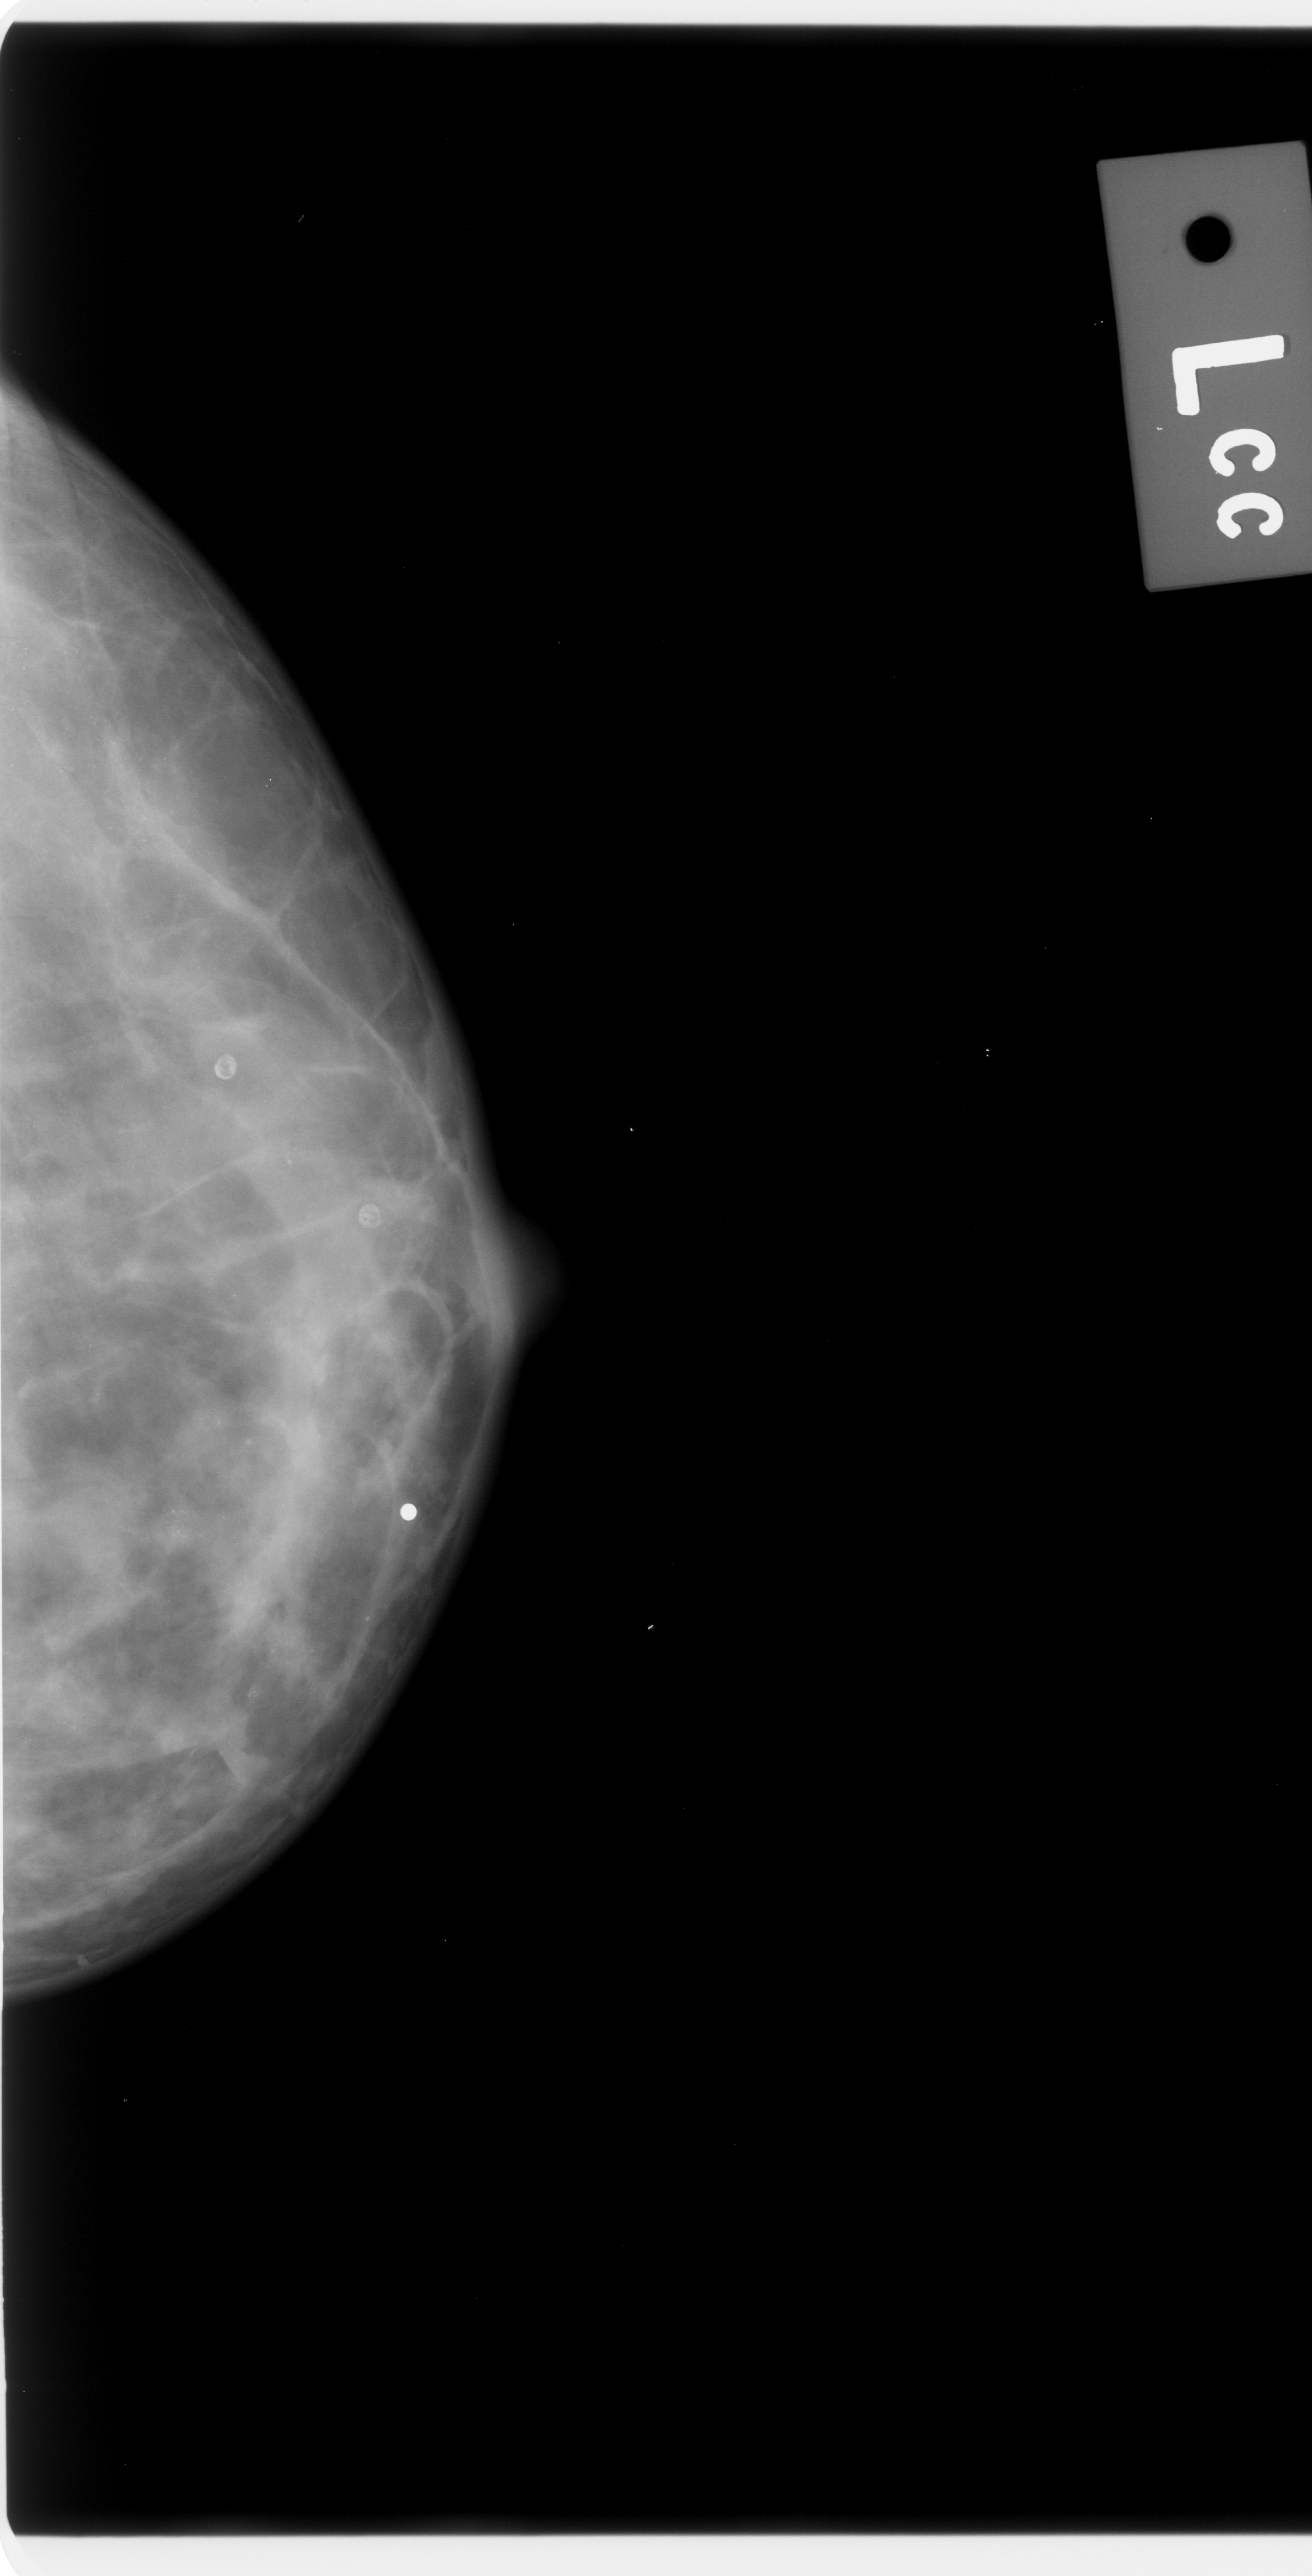
Scanned film-screen mammogram; left breast; CC view; BI-RADS breast density category 2 (scale 1–4).
Abnormality record for this image: calcifications, morphology amorphous, distribution diffusely scattered; BI-RADS assessment category 3; pathology result (as recorded, not read from the image): malignant.